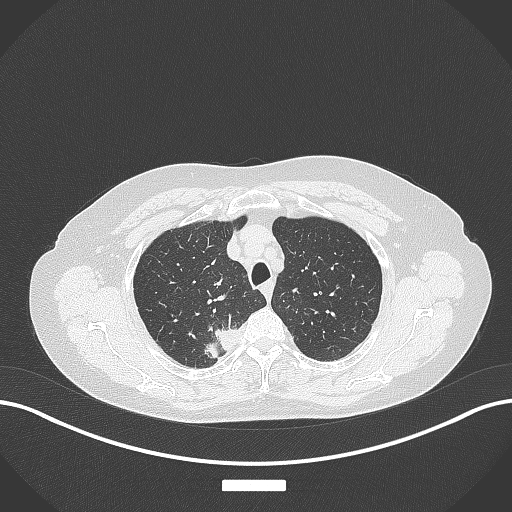
Chest CT, one axial slice. Position 317 of 357 along the scan axis. 120 kVp. Lung window (W 1500 / L -600 HU). 512 × 512 image matrix, field of view 400 × 400 mm. Female patient, age 62 years. From the clinical record (not read from this slice): clinical TNM (as recorded): T1c N1 M0.
Outlined on this slice (rectangle marked by the reading radiologist):
- lung tumour (recorded histology: squamous cell carcinoma): bounding box [x1, y1, x2, y2] px = [199, 311, 252, 361]